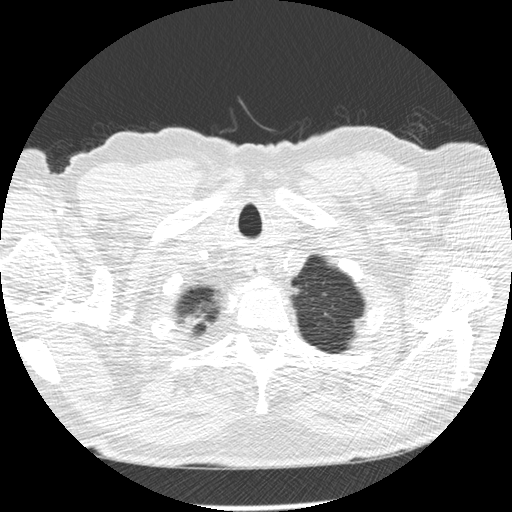
Chest CT (low-dose screening protocol), one axial image, second screening round (one year after baseline), lung window (W 1500 / L -600 HU), standard (soft-tissue) reconstruction kernel (STANDARD), slice 18 of 276 in the series, 512 × 512 image matrix. Male, age 73 years at enrolment.
Lesion marked by an expert reader, bounding box <340,307,381,345> (left, top, right, bottom; pixels). No non-calcified nodule or mass ≥4 mm was recorded by the screening reader at this exam. Official screen result: negative screen, minor abnormalities not suspicious for lung cancer. Later outcome: lung cancer diagnosed 457 days after this screen — adenocarcinoma, NOS, left upper lobe, poorly differentiated (G3), stage IB (AJCC 6th edition), 10 mm at pathology.